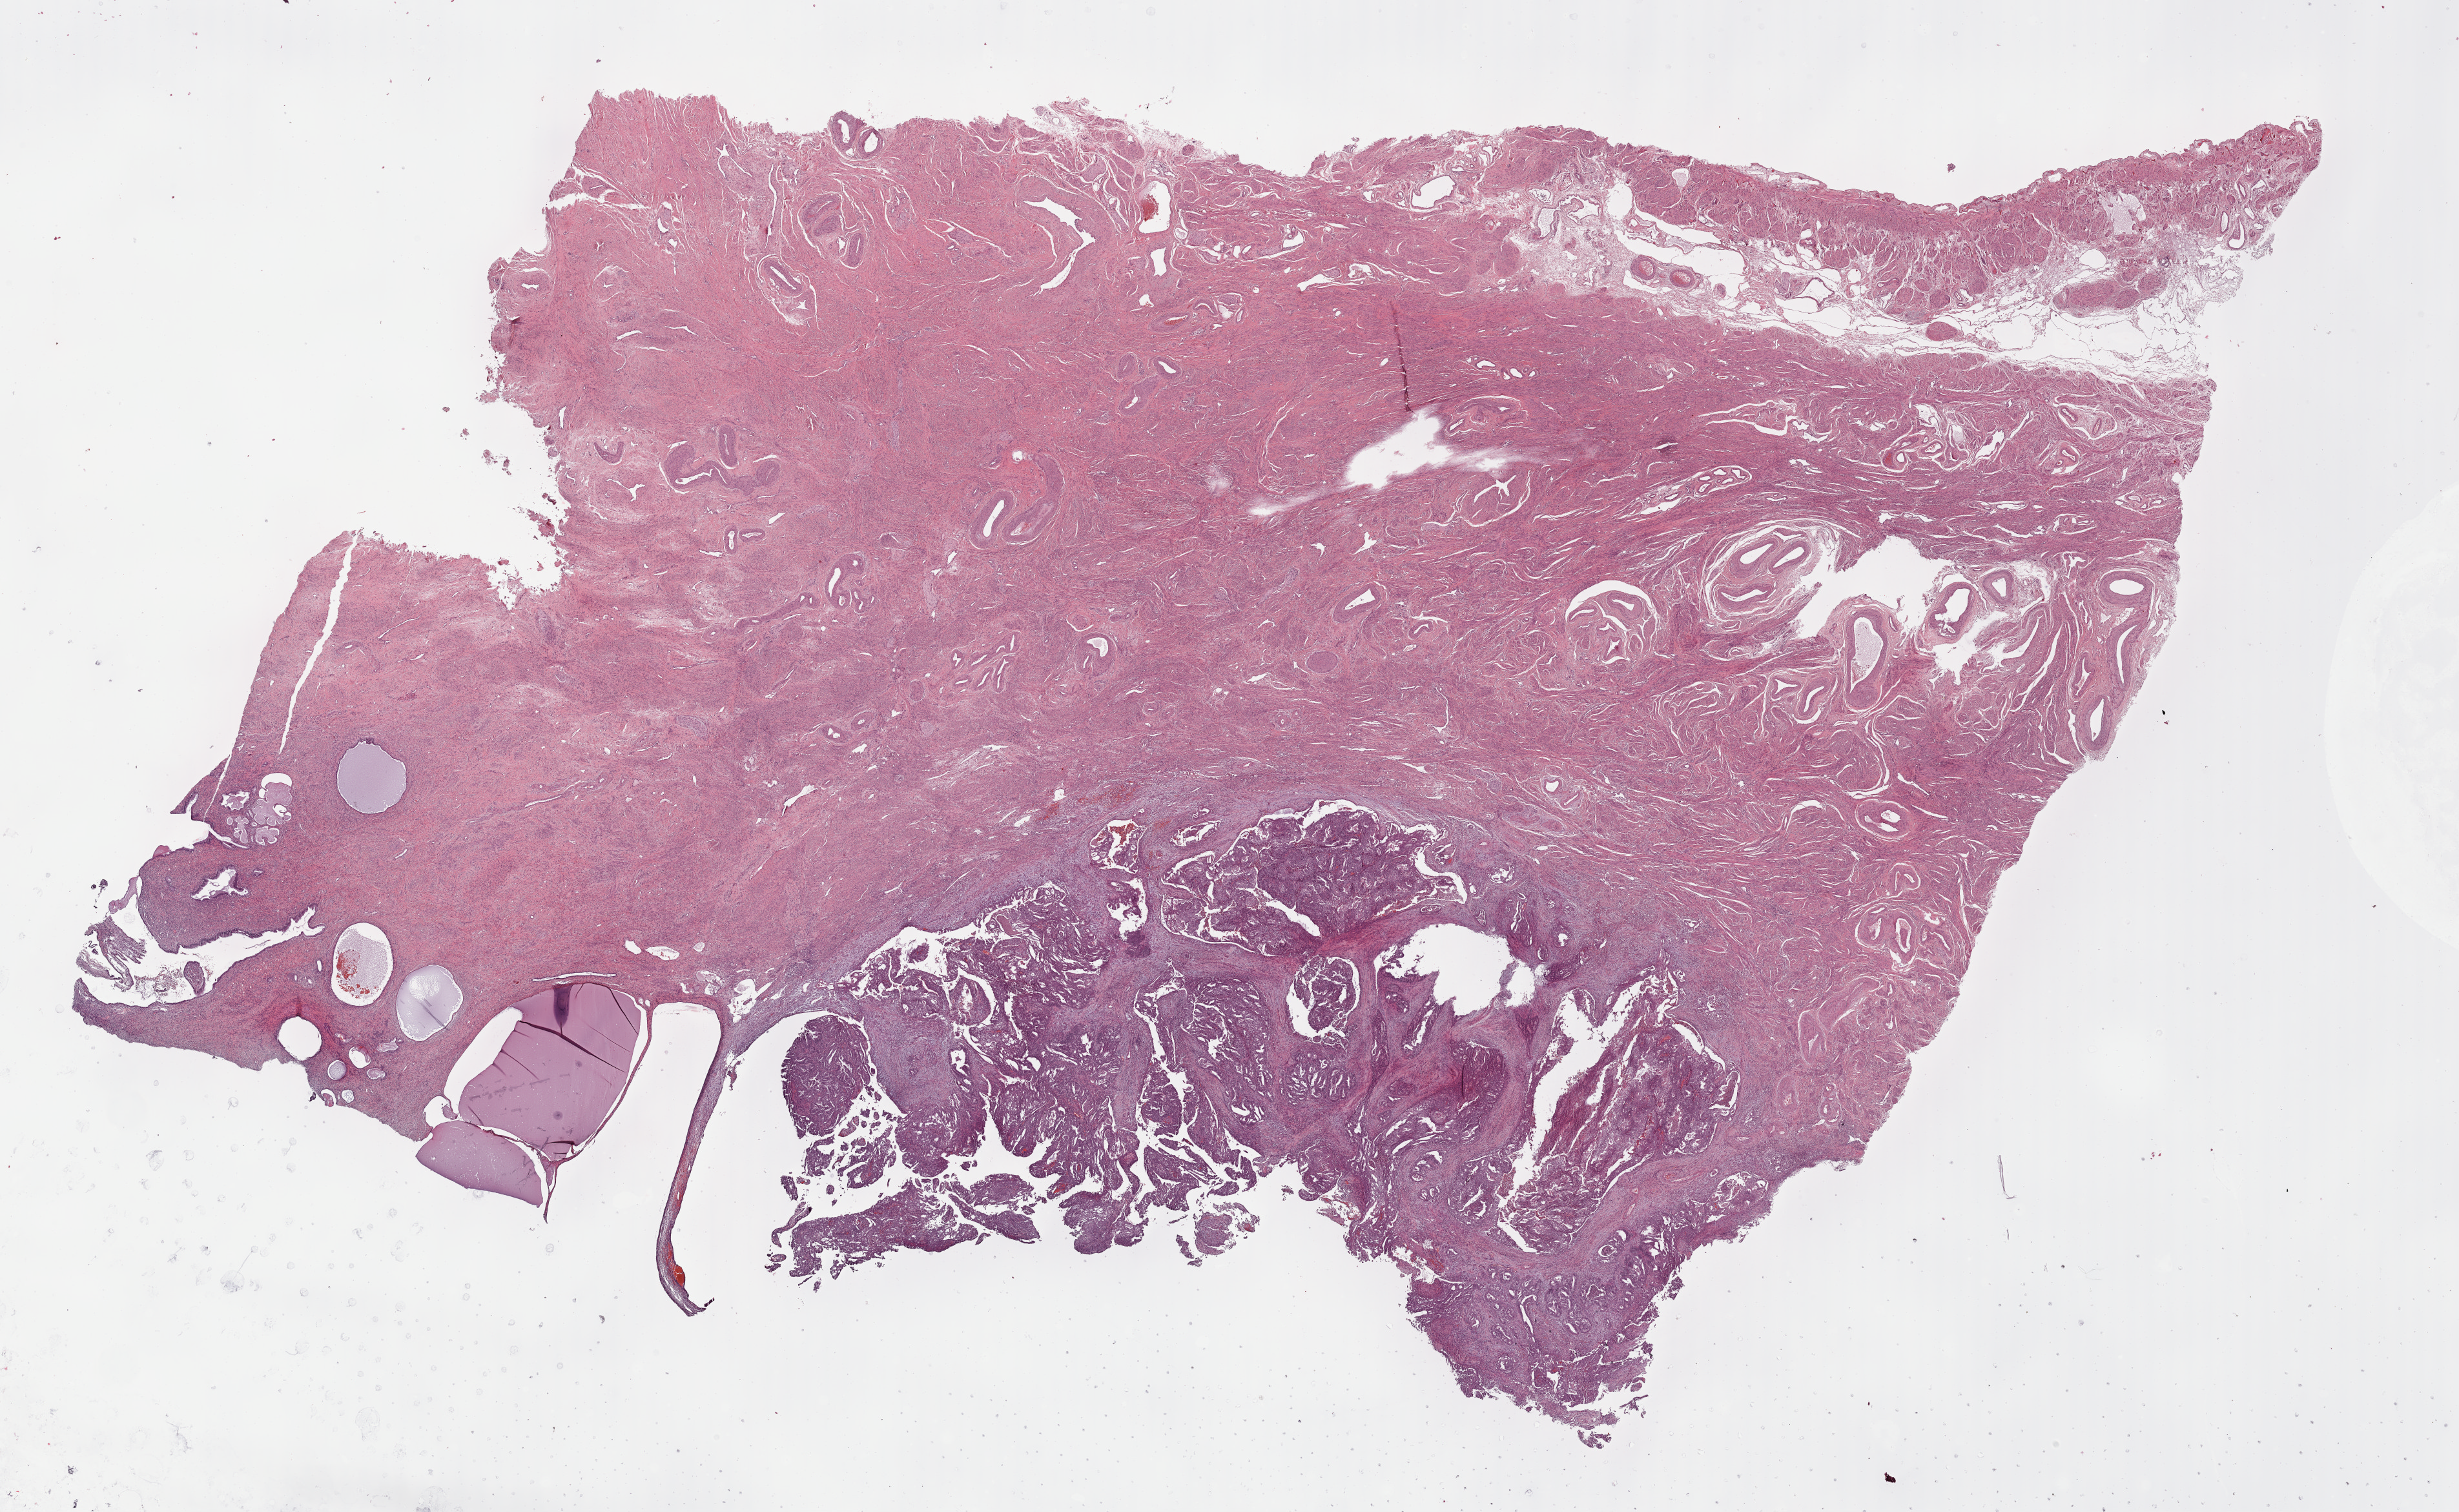
H&E-stained whole-slide image — low-resolution overview of the scanned area, about 30.0 x 18.5 mm, formalin-fixed paraffin-embedded (FFPE) diagnostic section, uterus, primary tumour sample. Female patient; age at initial diagnosis 60 years. Histologic grade: G2 (moderately differentiated).
FIGO stage: IIIA. Diagnosis: Endometrioid adenocarcinoma, NOS (endometrium). Lymph nodes positive (case pathology): 0 of 7 examined.